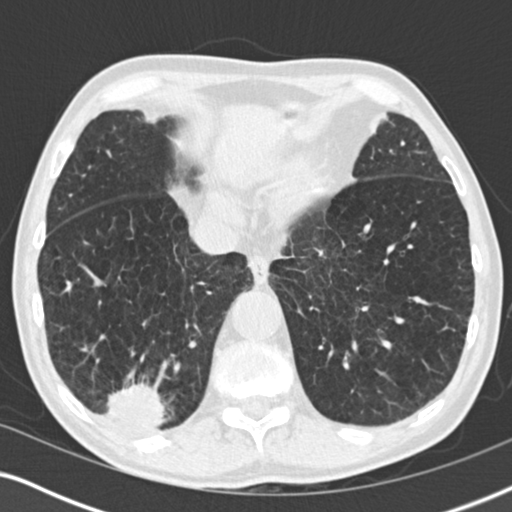
Axial slice from a low-dose chest CT screening exam, baseline screening round, lung window (W 1500 / L -600 HU), 2 mm slice thickness, 120 kVp, slice 139 of 196 in the series, 512 × 512 image matrix. Male participant, aged 64 years at enrolment. Former smoker at enrolment.
• Lesion marked by an expert reader, bounding box (x1, y1, x2, y2) in pixels: (83, 368, 179, 449).
• The screening reader recorded 3 non-calcified nodules or masses ≥4 mm on this exam (lingula, lingula, right lower lobe); which of them this box marks is not recorded.
• Participant outcome: lung cancer diagnosed 27 days after this screen — squamous cell carcinoma, NOS, right lower lobe, moderately differentiated (G2), stage IV (AJCC 6th edition), 40 mm at pathology.